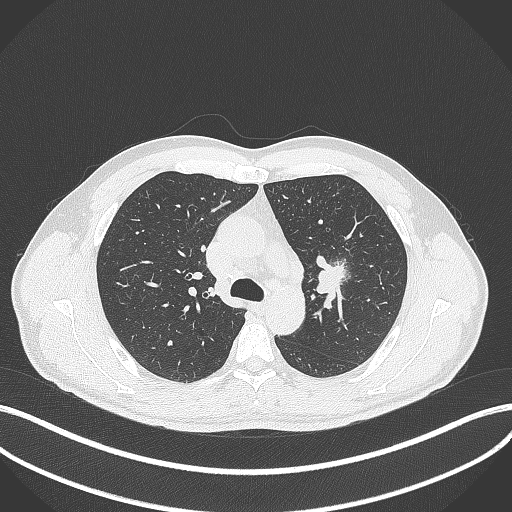
Chest CT, one axial slice; position 288 of 392 along the scan axis; lung window (W 1500 / L -600 HU); 512 × 512 image matrix. Patient: male, 50 years. Case-level facts recorded for this patient, not image findings: clinical TNM (as recorded): T1c N1 M1b.
Outlined on this slice (rectangle marked by the reading radiologist):
- lung tumour (recorded histology: squamous cell carcinoma): box from (x=313, y=252) to (x=348, y=295) px